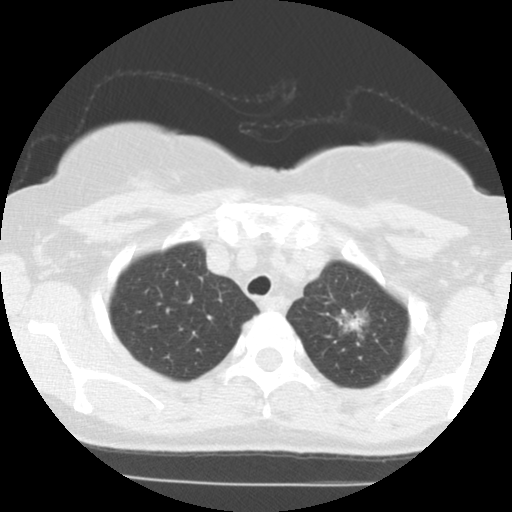
Axial slice from a low-dose chest CT screening exam, baseline screening round, lung window (W 1500 / L -600 HU), 2.5 mm slice thickness, standard (soft-tissue) reconstruction kernel (STANDARD), slice 101 of 123 in the series. Female, age 61 years at enrolment. Former smoker at enrolment.
Expert reader's lesion annotation, bounding box (x1, y1, x2, y2) in pixels: (322, 300, 383, 351). The screening reader recorded 2 non-calcified nodules or masses ≥4 mm on this exam (right lower lobe, left upper lobe); which of them this box marks is not recorded. Participant outcome: lung cancer diagnosed 79 days after this screen — adenocarcinoma, NOS, left upper lobe, stage IIIB (AJCC 6th edition), 15 mm at pathology.